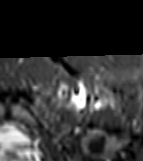
MRI of an extremity soft-tissue mass, one axial slice; position 59 of 81 along the scan axis; STIR; MR volume resampled by the dataset authors to the PET/CT grid (not the native acquisition matrix); 3.27 mm slice thickness; 143 × 161 image matrix. Female patient. From the clinical record (not read from this slice): histological type: myxofibrosarcoma; grade: intermediate; site of the primary tumour: left thigh.
Outlined on this slice (expert contour drawn on MRI and transferred to this co-registered scan by the dataset authors):
- gross tumour volume including surrounding oedema: bounding box [x1, y1, x2, y2] px = [58, 83, 109, 105]